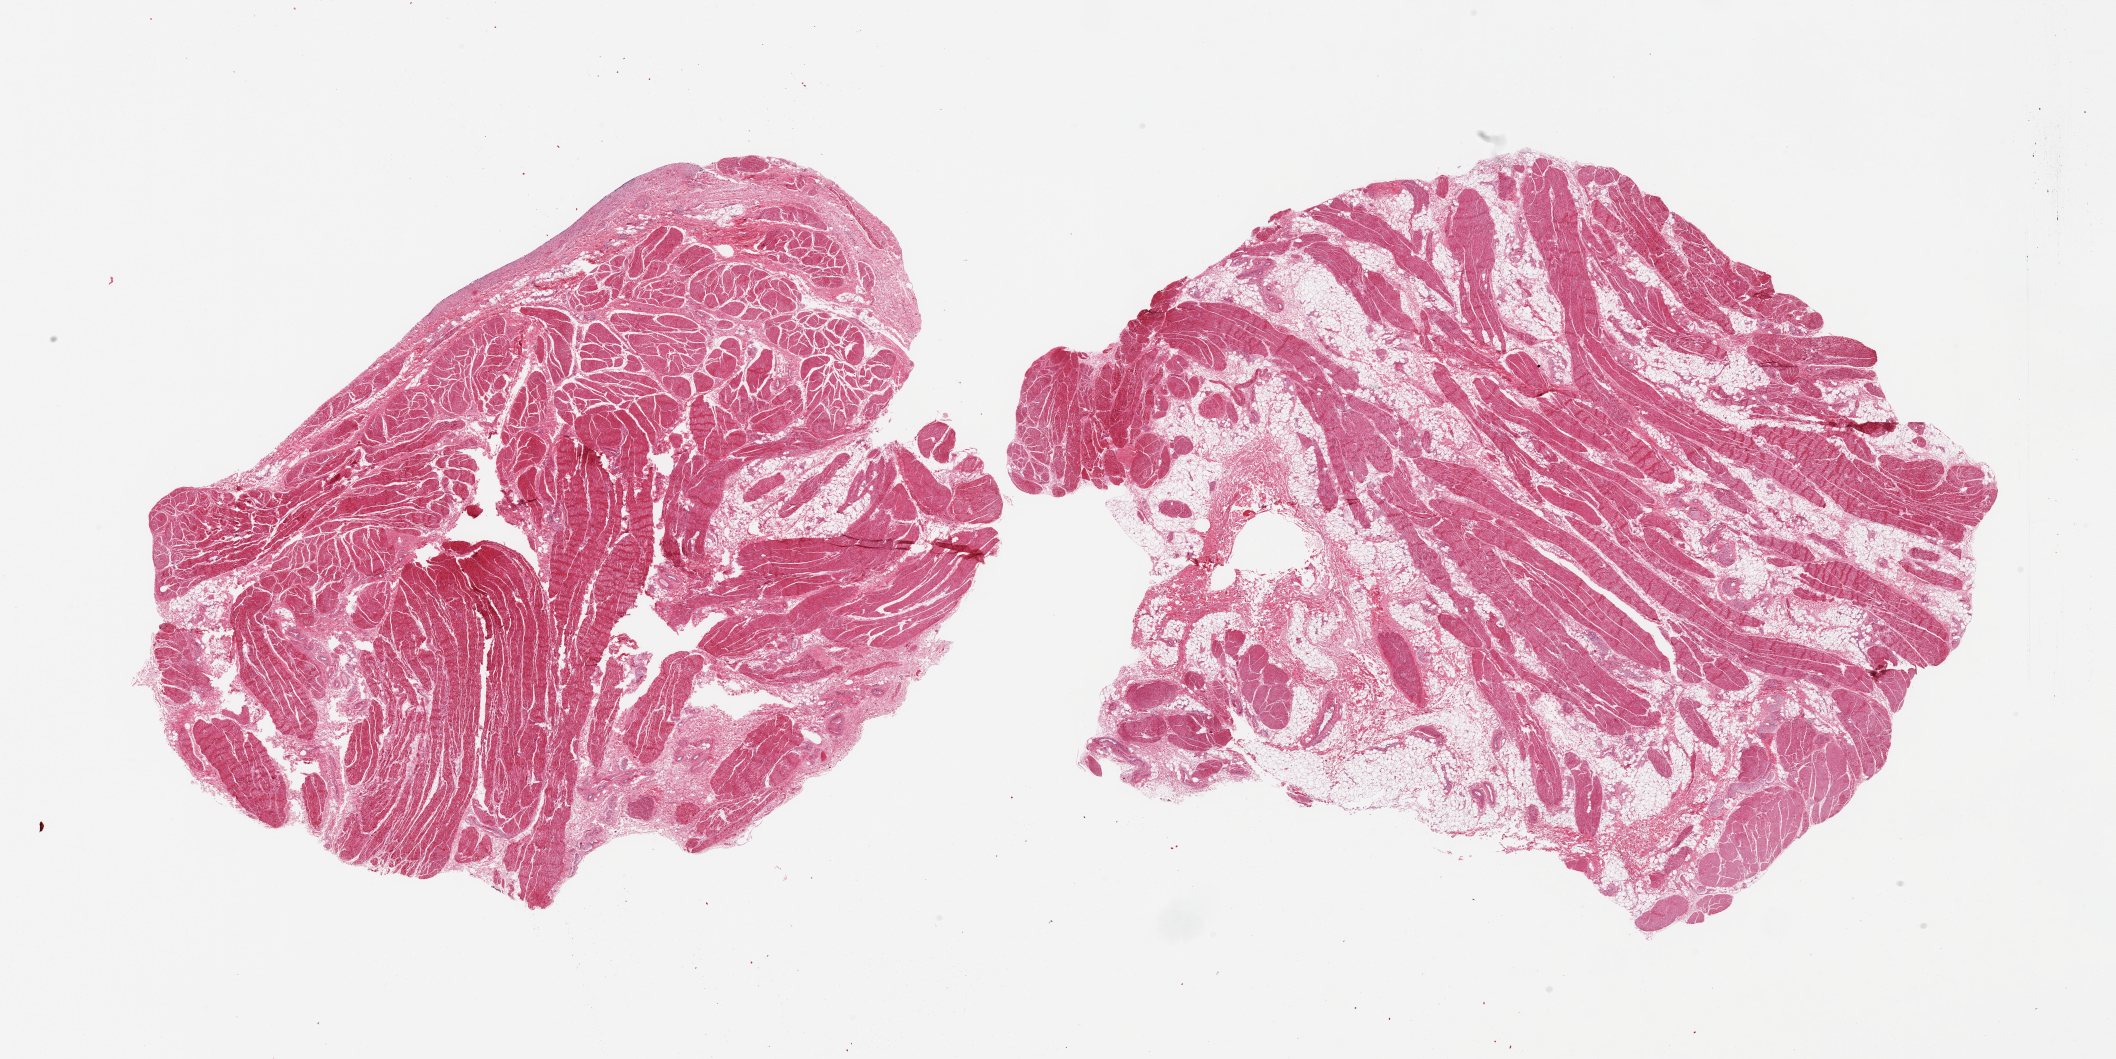
H&E whole-slide image, a low-resolution overview of the entire scanned area, about 33.5 x 16.8 mm (slide scanned at 20x), PAXgene-fixed, paraffin-embedded tissue, sampled site (target tissue): prostate, donor tissue sample.
Reviewer comment on this tissue sample: 2 pieces; fat, peripheral nerve, and skeletal muscle; no prostate present.